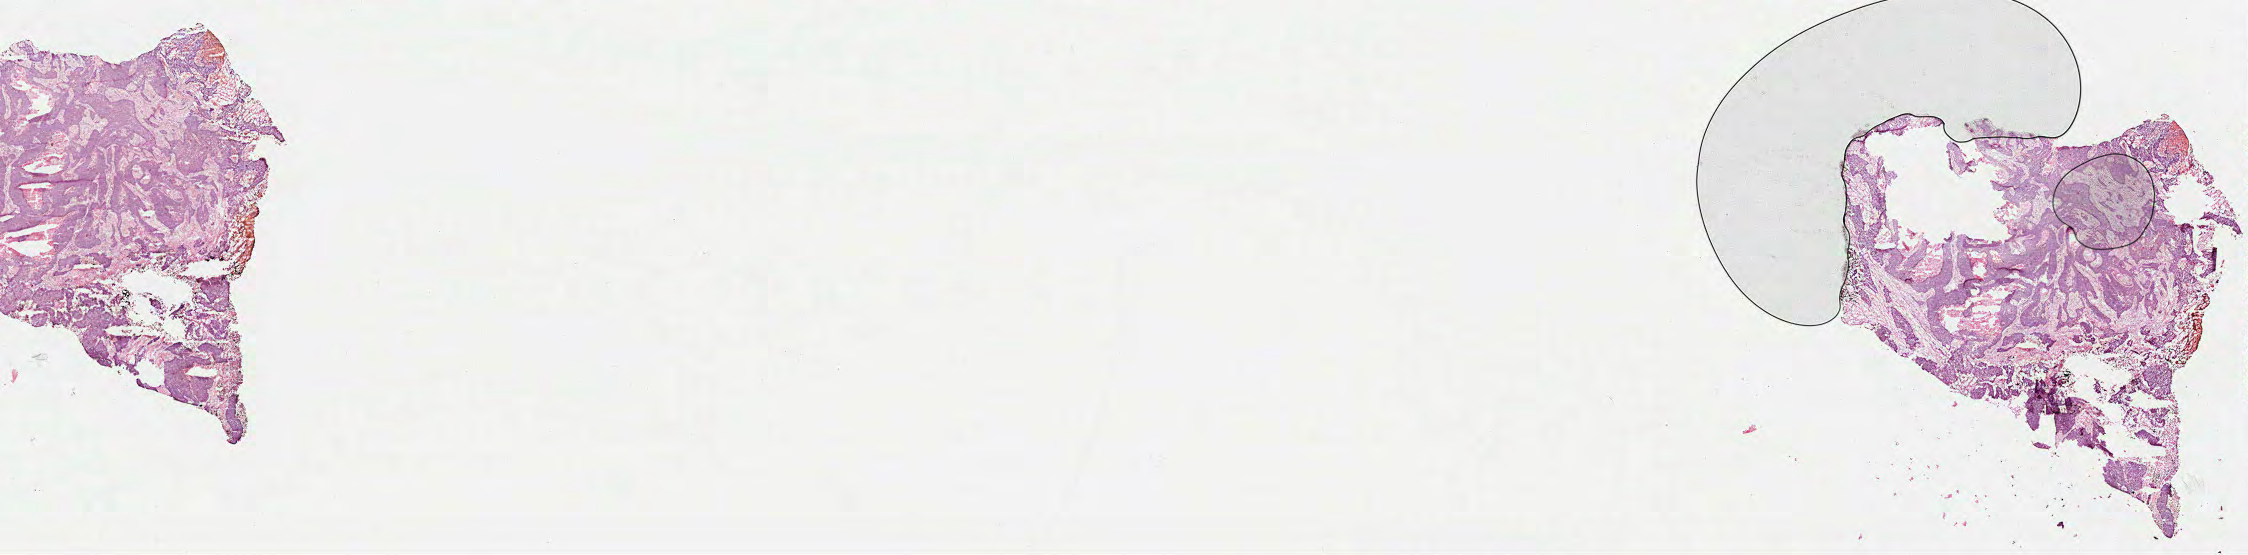
Whole-slide histology image, Hematoxylin and eosin (H&E) stained, a low-resolution overview of the entire scanned area, about 36.3 x 9.0 mm, formalin-fixed paraffin-embedded (FFPE) diagnostic section, head and neck, primary tumour sample. Male, age 50 years at initial diagnosis. Histologic grade: GX (grade cannot be assessed).
Diagnosis: Squamous cell carcinoma, NOS (base of tongue, NOS). AJCC pathologic stage: III (7th edition). Laterality: right.